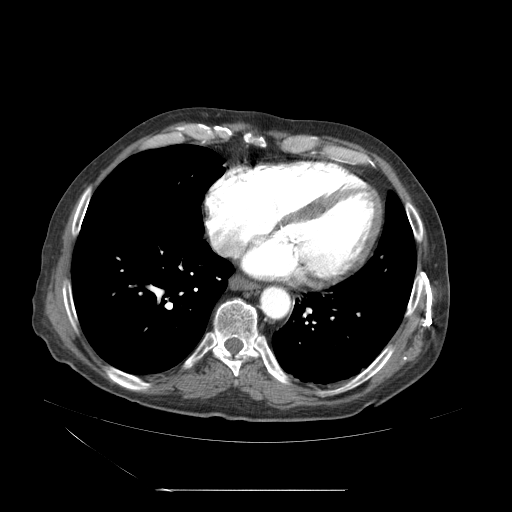
Contrast-enhanced abdominal CT (liver protocol), one axial slice. Position 66 of 71 along the scan axis. Reconstruction kernel STANDARD. 120 kVp. Soft-tissue window (W 400 / L 40 HU). 2.5 mm slice thickness. 512 × 512 image matrix, field of view 440 × 440 mm. Case-level facts recorded for this patient, not image findings: diagnosis: hepatocellular carcinoma (patient treated with transarterial chemoembolisation; whether this scan precedes or follows treatment is not stated here); TNM stage (as recorded): Stage-II; Child-Pugh class: A; tumour nodularity: multinodular.
Structures marked on this image (semi-automatically segmented with operator editing):
- abdominal aorta: bounding box [x1, y1, x2, y2] px = [260, 287, 289, 319]